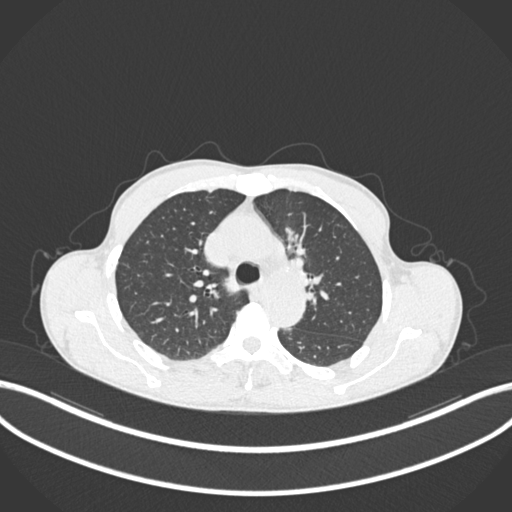
Chest CT, one axial slice. Position 138 of 211 along the scan axis. Lung window (W 1500 / L -600 HU). 1 mm slice thickness. 512 × 512 image matrix, field of view 400 × 400 mm. Patient: male, 58 years. Case-level facts recorded for this patient, not image findings: clinical TNM (as recorded): T1c N1 M0.
Structures marked on this image (bounding box drawn by a radiologist):
- lung tumour (recorded histology: adenocarcinoma): bounding box (x1, y1, x2, y2) in pixels: (278, 218, 314, 277)